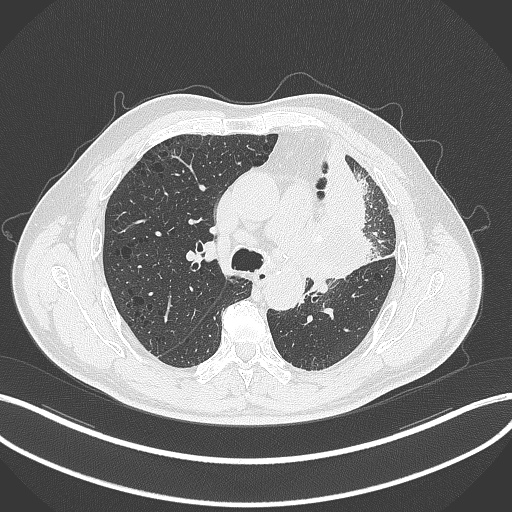
Chest CT, one axial slice; position 198 of 297 along the scan axis; reconstruction kernel B70f; lung window (W 1500 / L -600 HU); 1 mm slice thickness; 512 × 512 image matrix. Male patient, age 68 years. From the clinical record (not read from this slice): clinical TNM (as recorded): T3 N3 M1.
Structures marked on this image (bounding box drawn by a radiologist):
- lung tumour (recorded histology: adenocarcinoma): bounding box <299,142,374,286> (left, top, right, bottom; pixels)